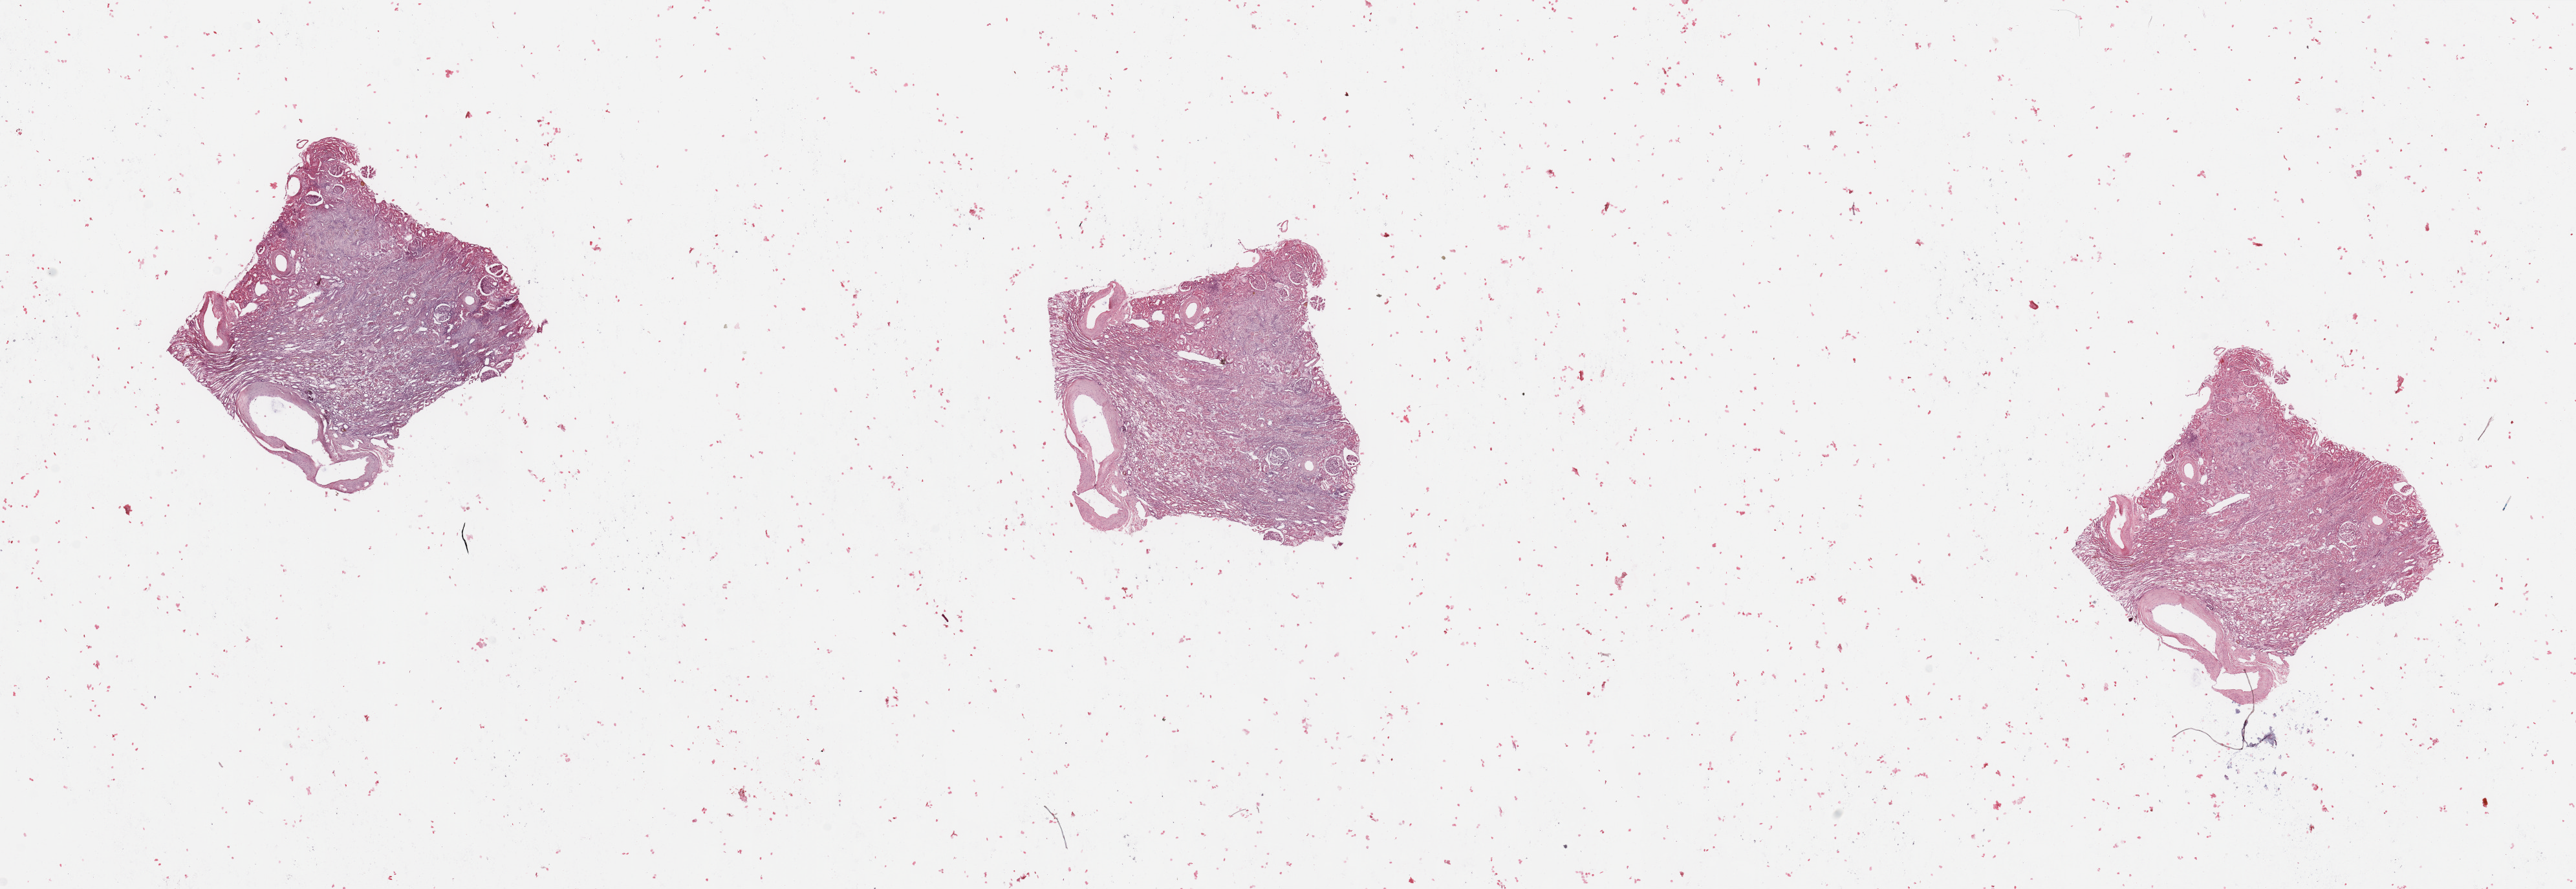
Digitized H&E tissue section (whole slide) — whole scanned area (about 31.5 x 10.9 mm) shown as a low-resolution overview, normal (non-tumour) tissue sample, sampled site: kidney. Male, 65 y/o.
This section: normal (non-tumour) tissue from the same patient. Patient diagnosis: Renal cell carcinoma, NOS.